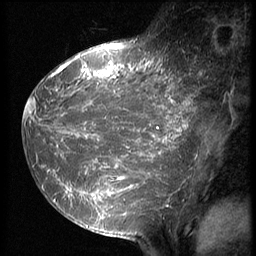
Breast MRI (dynamic contrast-enhanced), one sagittal slice; position 24 of 64 along the scan axis; 3 images stored at this slice position (order not interpretable as contrast timing); 1.5 T; TE 4.2 ms, TR 9 ms; 256 × 256 image matrix. Female patient, age 39 years. Case-level facts recorded for this patient, not image findings: setting: breast cancer imaged before/during neoadjuvant chemotherapy; receptor status: HER2-positive.
Structures marked on this image (semi-automatically segmented with operator editing):
- analysis volume of interest (the breast-tissue region the enhancement analysis was run in; not a lesion): bounding box <23,47,203,239> (left, top, right, bottom; pixels)
- tumour enhancement mask (voxels above the 140 % enhancement threshold inside the analysis volume of interest): <23,47,197,219>